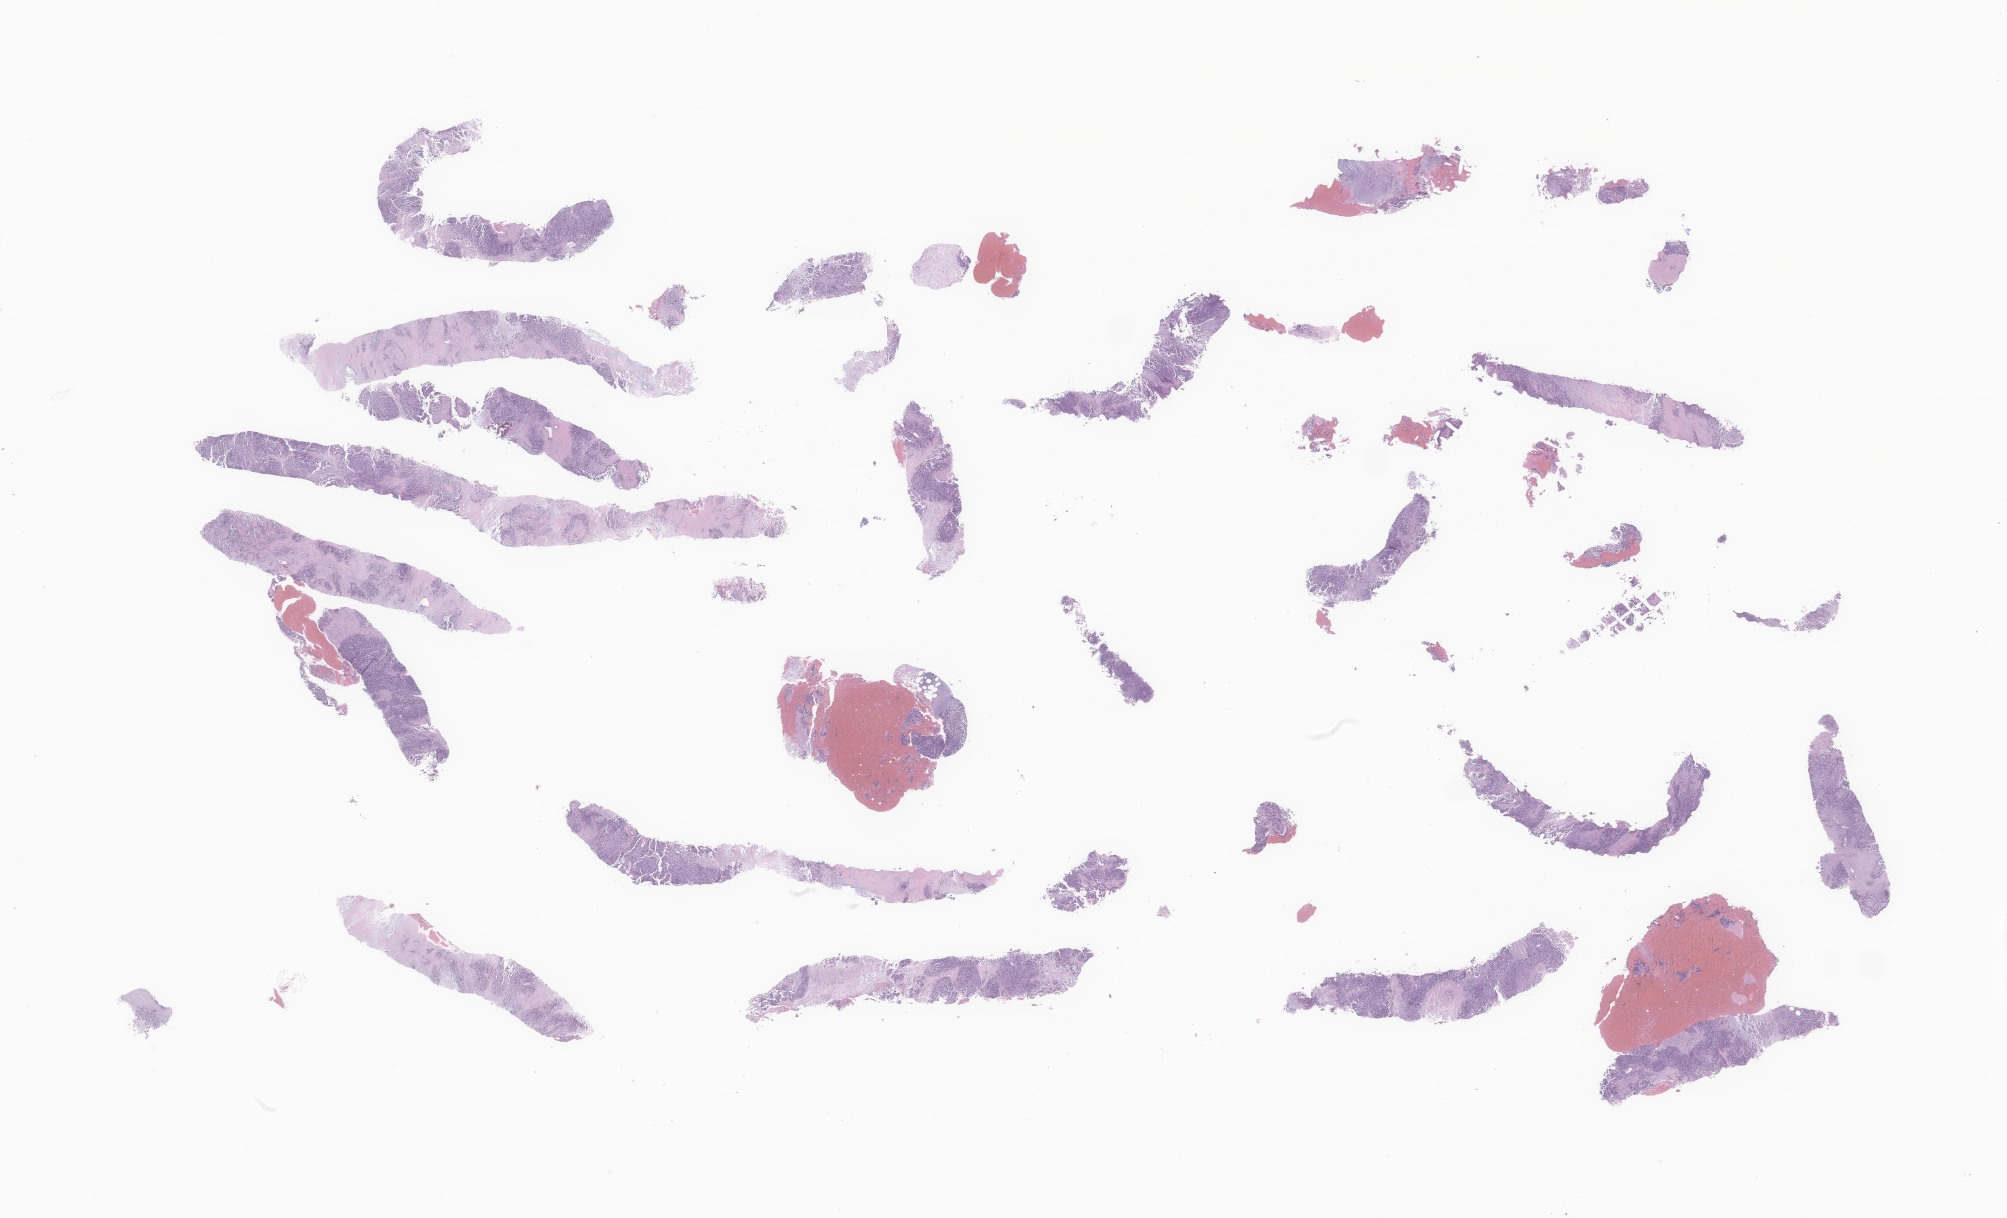
Digitized haematoxylin and eosin-stained section of tumor tissue from the pelvis, a low-resolution overview of the entire scanned area, about 33.9 x 20.5 mm, formalin-fixed paraffin-embedded section. Patient: female, age 172 months (14 years 4 months).
- diagnosis: Desmoplastic small round cell tumor